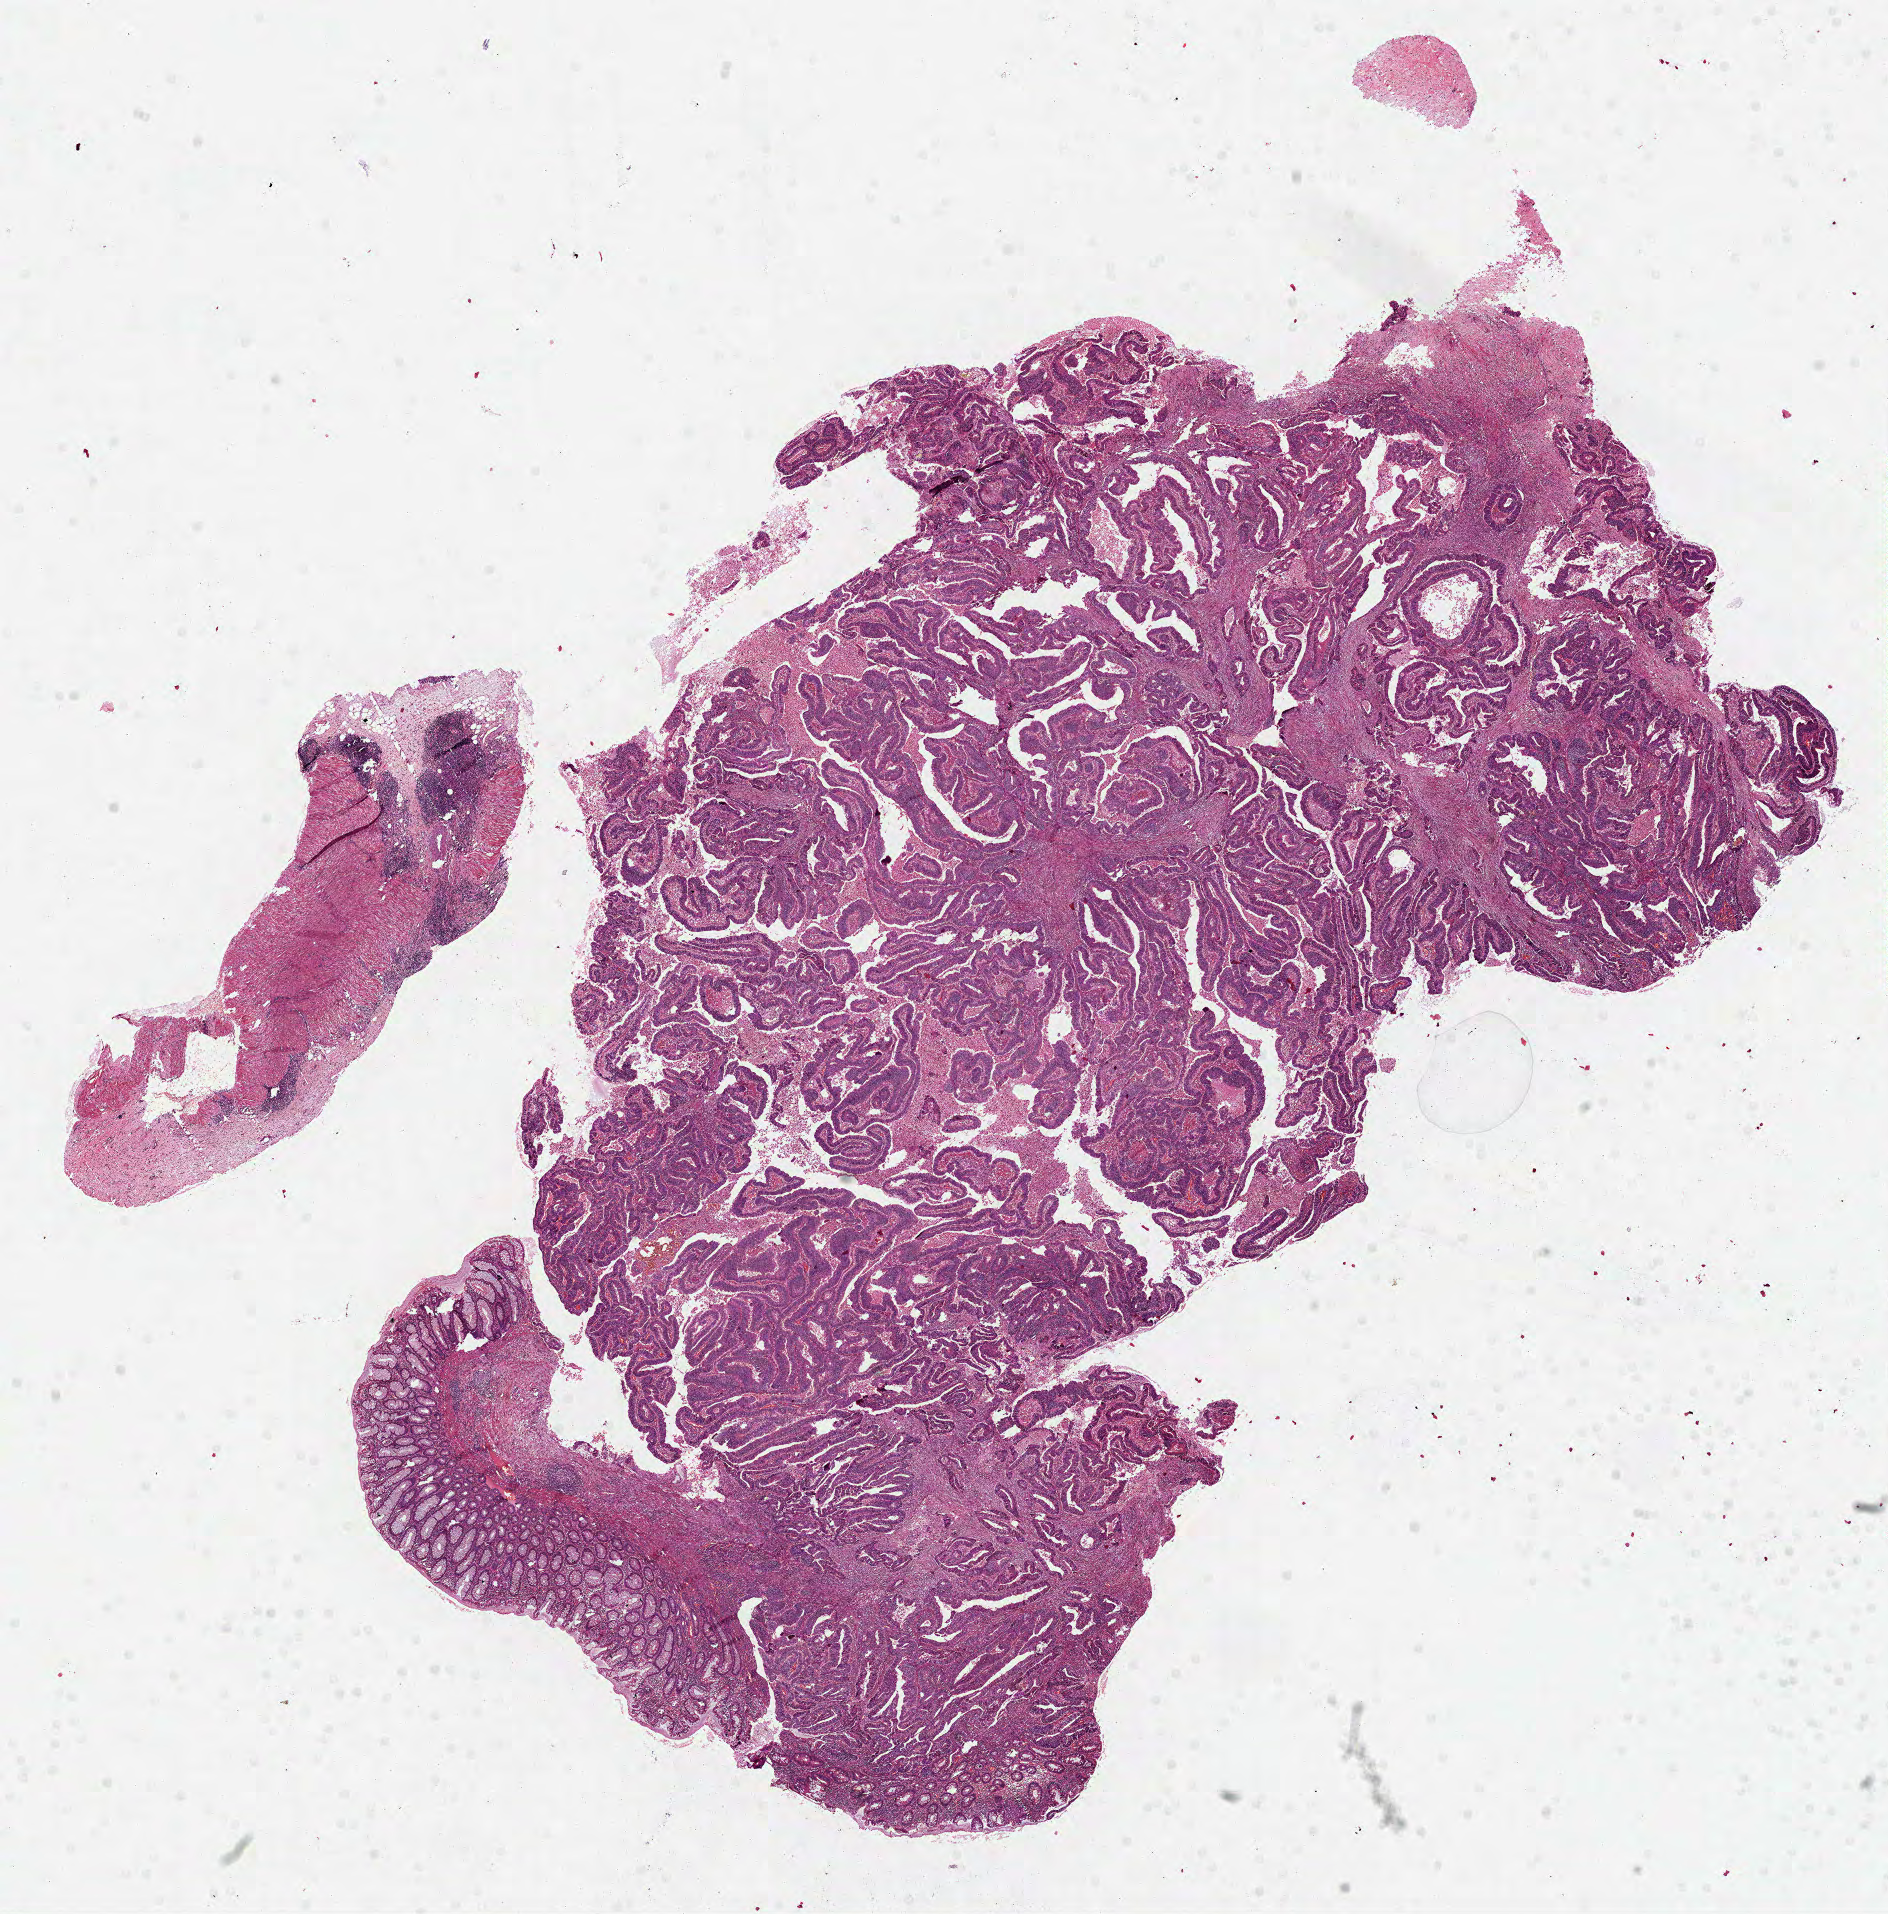
Whole-slide histology image, H&E-stained, shown as a low-resolution overview of the whole scanned area (about 15.2 x 15.4 mm); formalin-fixed paraffin-embedded (FFPE) diagnostic section; primary tumour sample from the colon. Female patient; age at initial diagnosis 54 years.
Histologic diagnosis: Adenocarcinoma, NOS. AJCC pathologic stage: IIA.